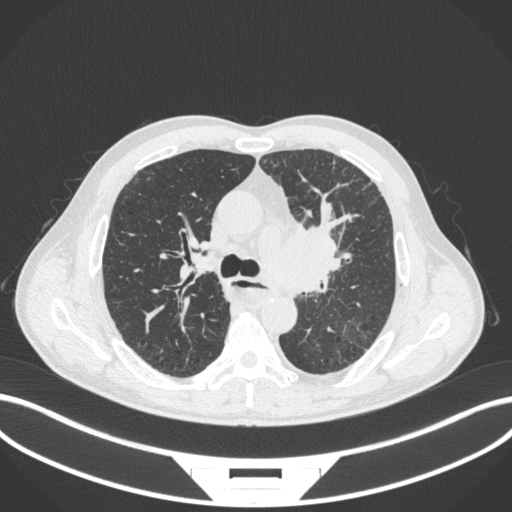
Chest CT, one axial slice; slice 251 of 411 in the series (ordered by position); reconstruction kernel B31f; lung window (W 1500 / L -600 HU); 512 × 512 image matrix. Male patient, age 57 years. Case-level facts recorded for this patient, not image findings: clinical TNM (as recorded): T2a N1 M0.
Annotated regions visible in this slice (bounding box drawn by a radiologist):
- lung tumour (recorded histology: squamous cell carcinoma): bounding box (x1, y1, x2, y2) in pixels: (258, 221, 347, 296)